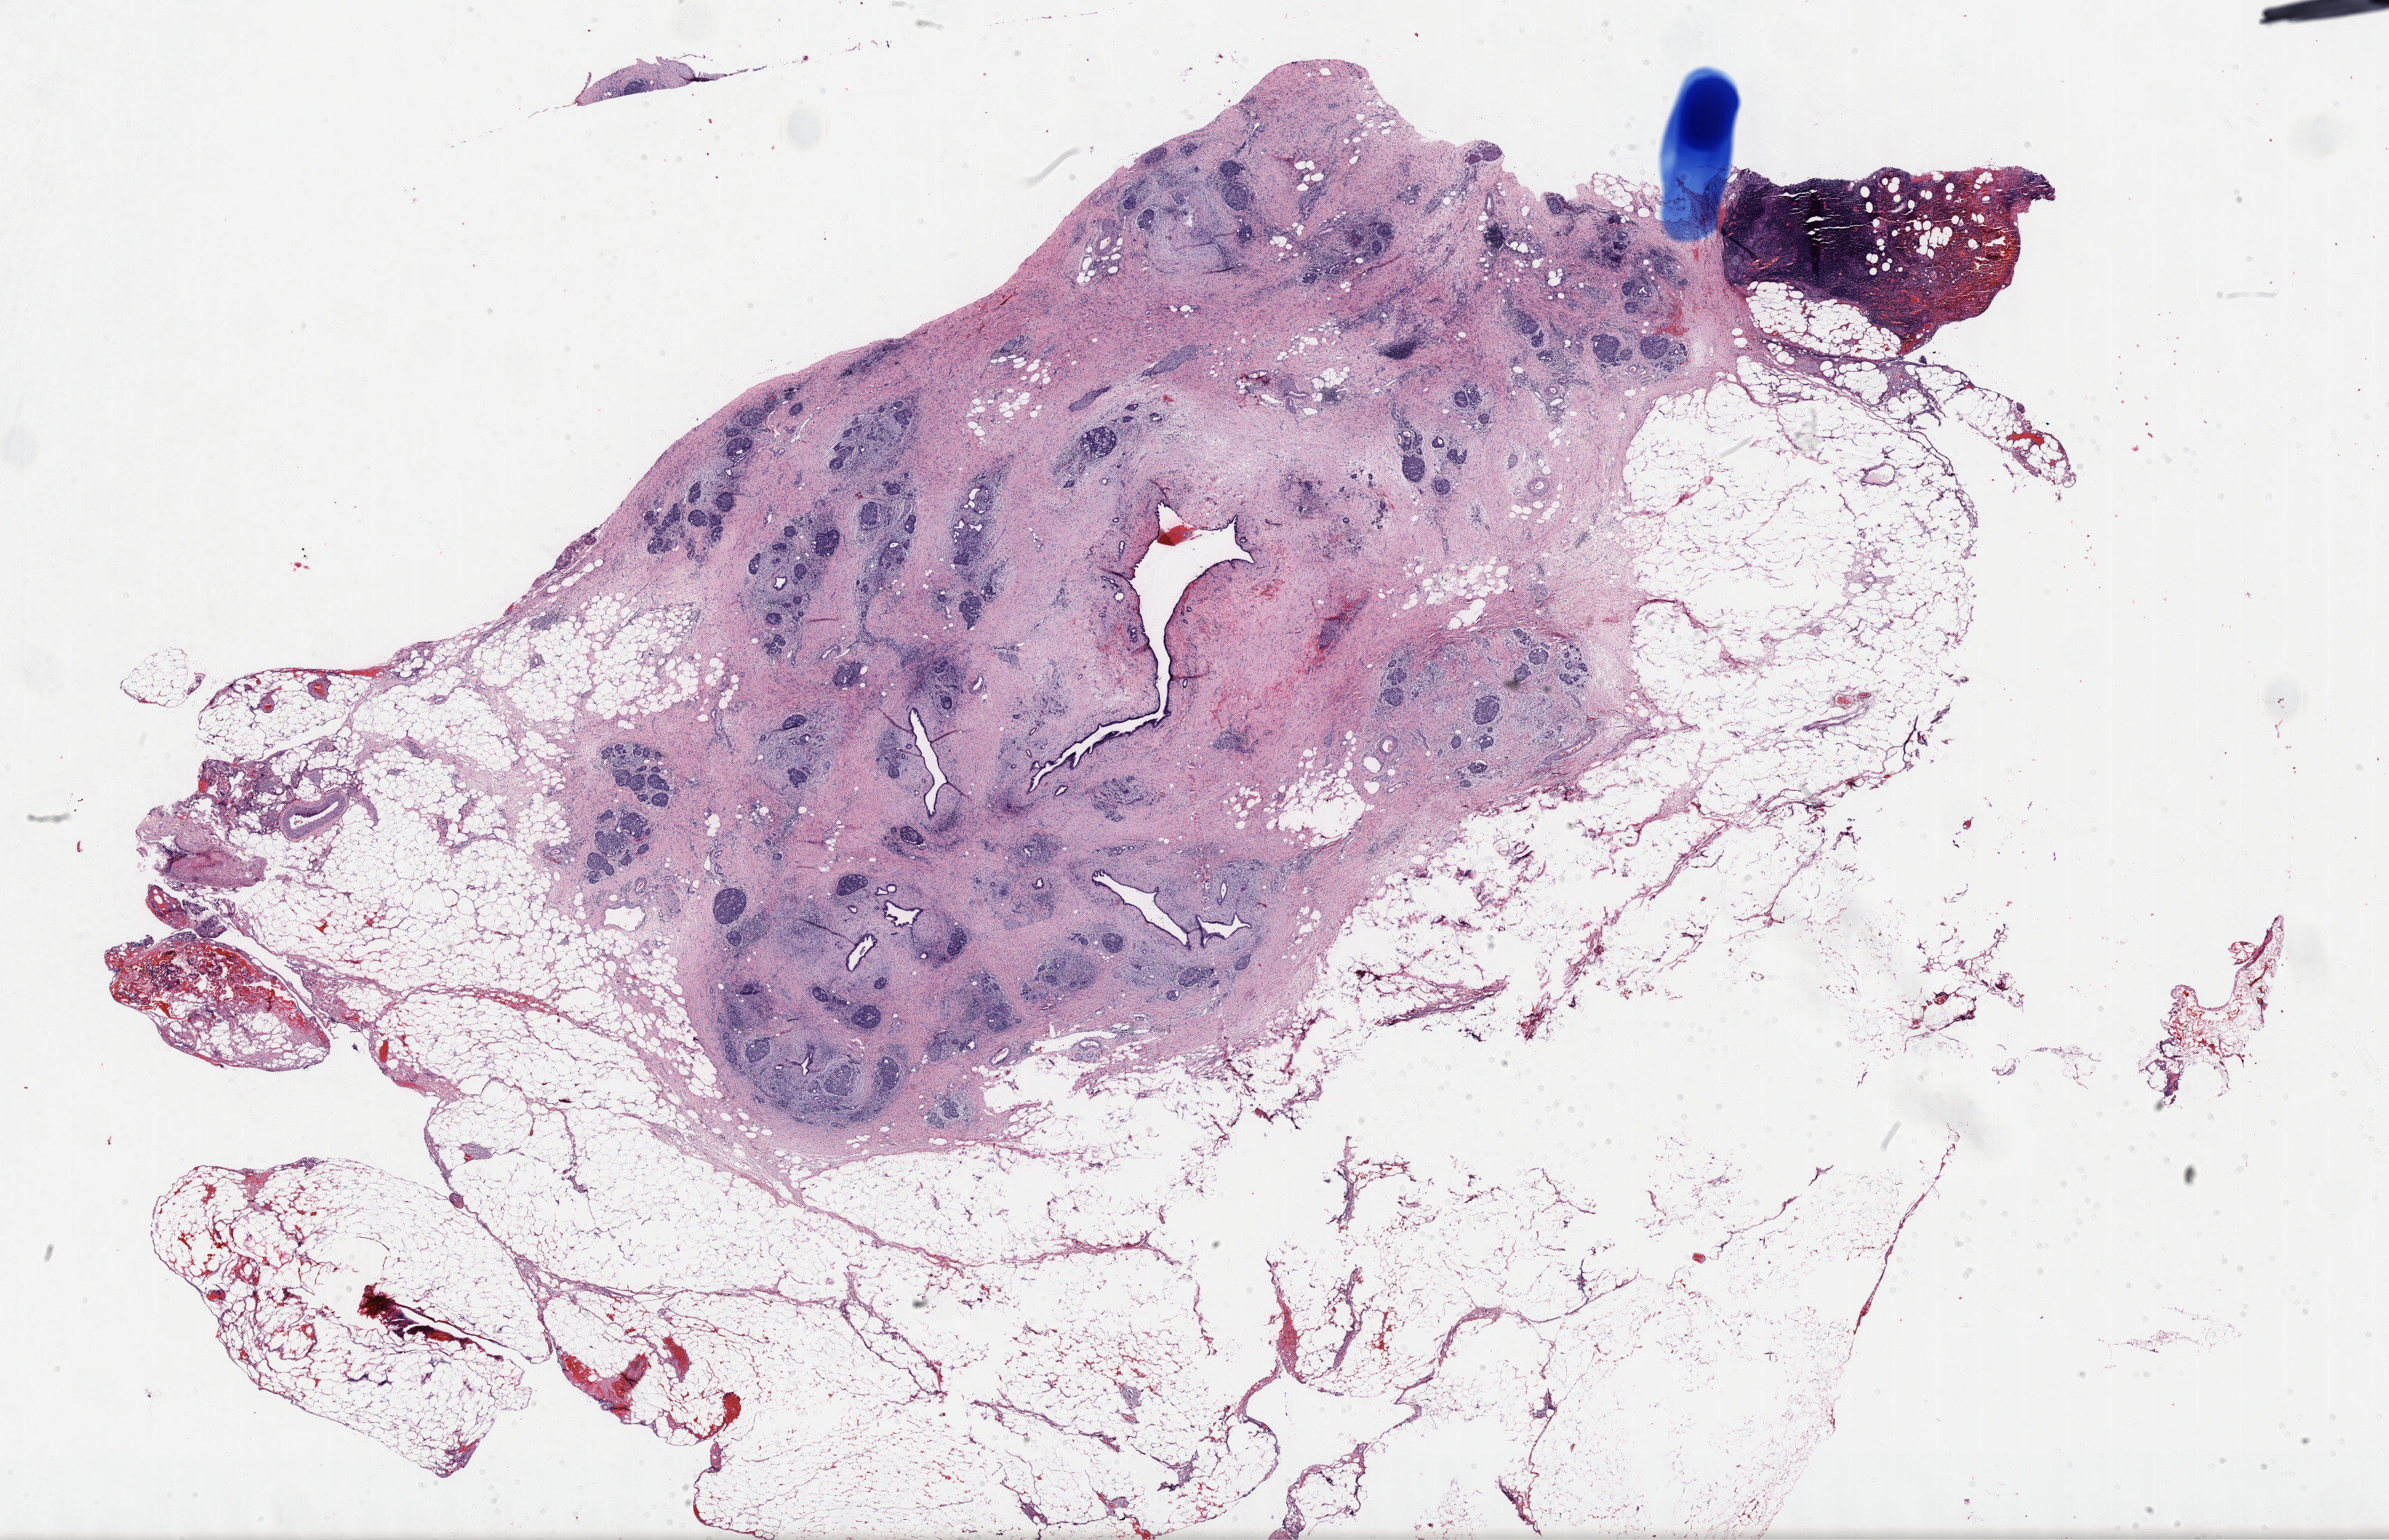
H&E whole-slide image — a low-resolution overview of the entire scanned area, about 27.7 x 17.9 mm (slide scanned at 40x). FFPE section. Pancreas, primary tumour sample. Patient: female, age at initial diagnosis 48 years. Histologic grade: G3 (poorly differentiated).
Lymph nodes positive (case pathology): 2 of 11 examined. AJCC pathologic stage: IIB (7th edition). Diagnosis: Infiltrating duct carcinoma, NOS (head of pancreas).